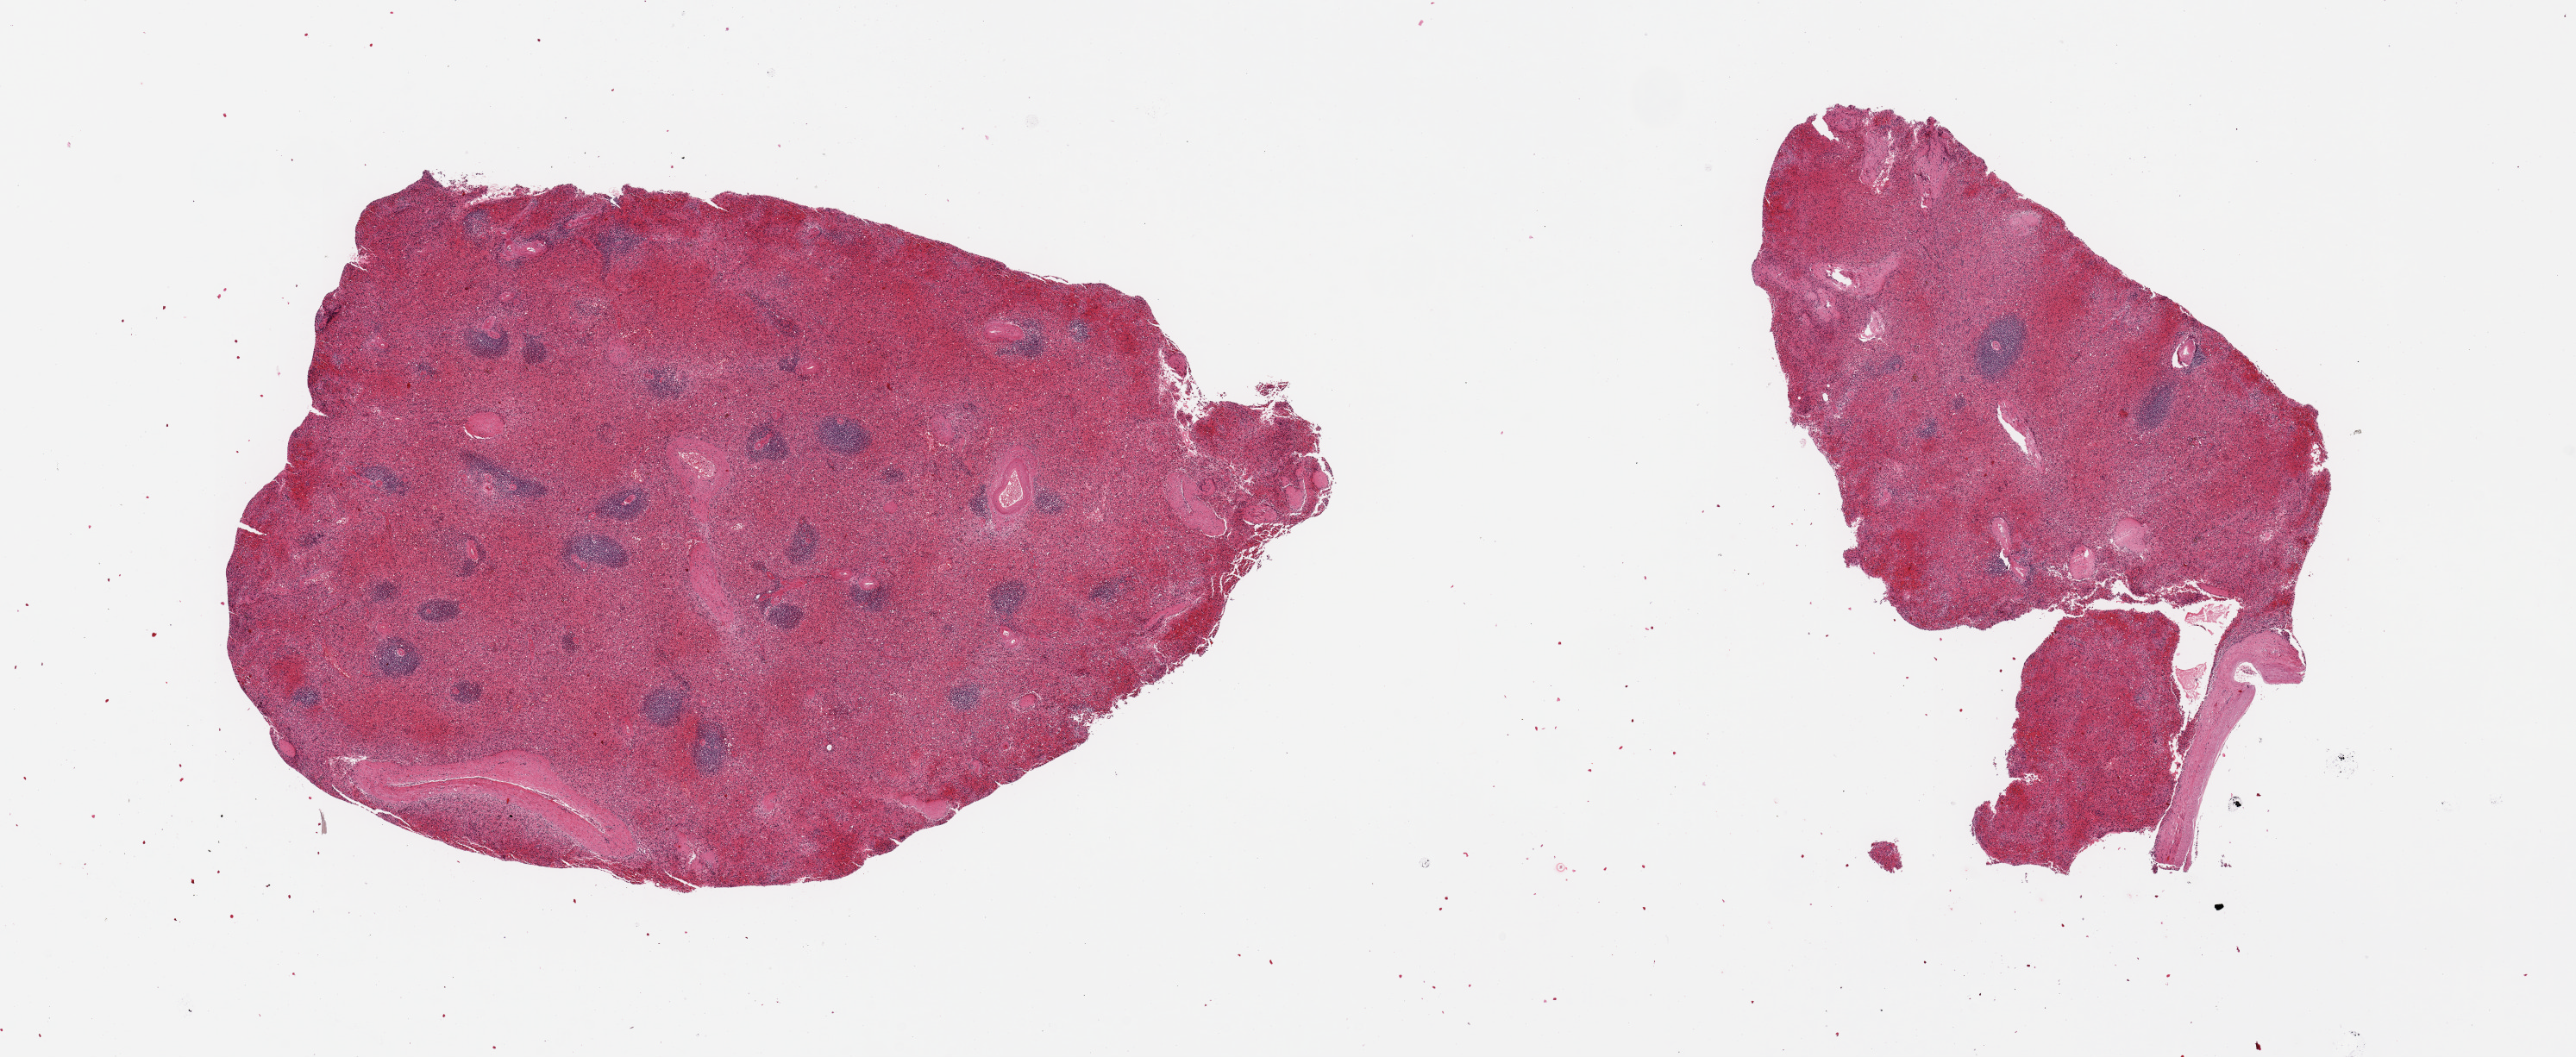
Whole-slide image, hematoxylin and eosin (H&E) stain — shown as a low-resolution overview of the whole scanned area (about 23.6 x 9.7 mm). PAXgene-fixed, paraffin-embedded tissue. Section of spleen (target tissue). Donor tissue sample. Male donor.
- review note (as recorded): 2 pieces, moderate congestion